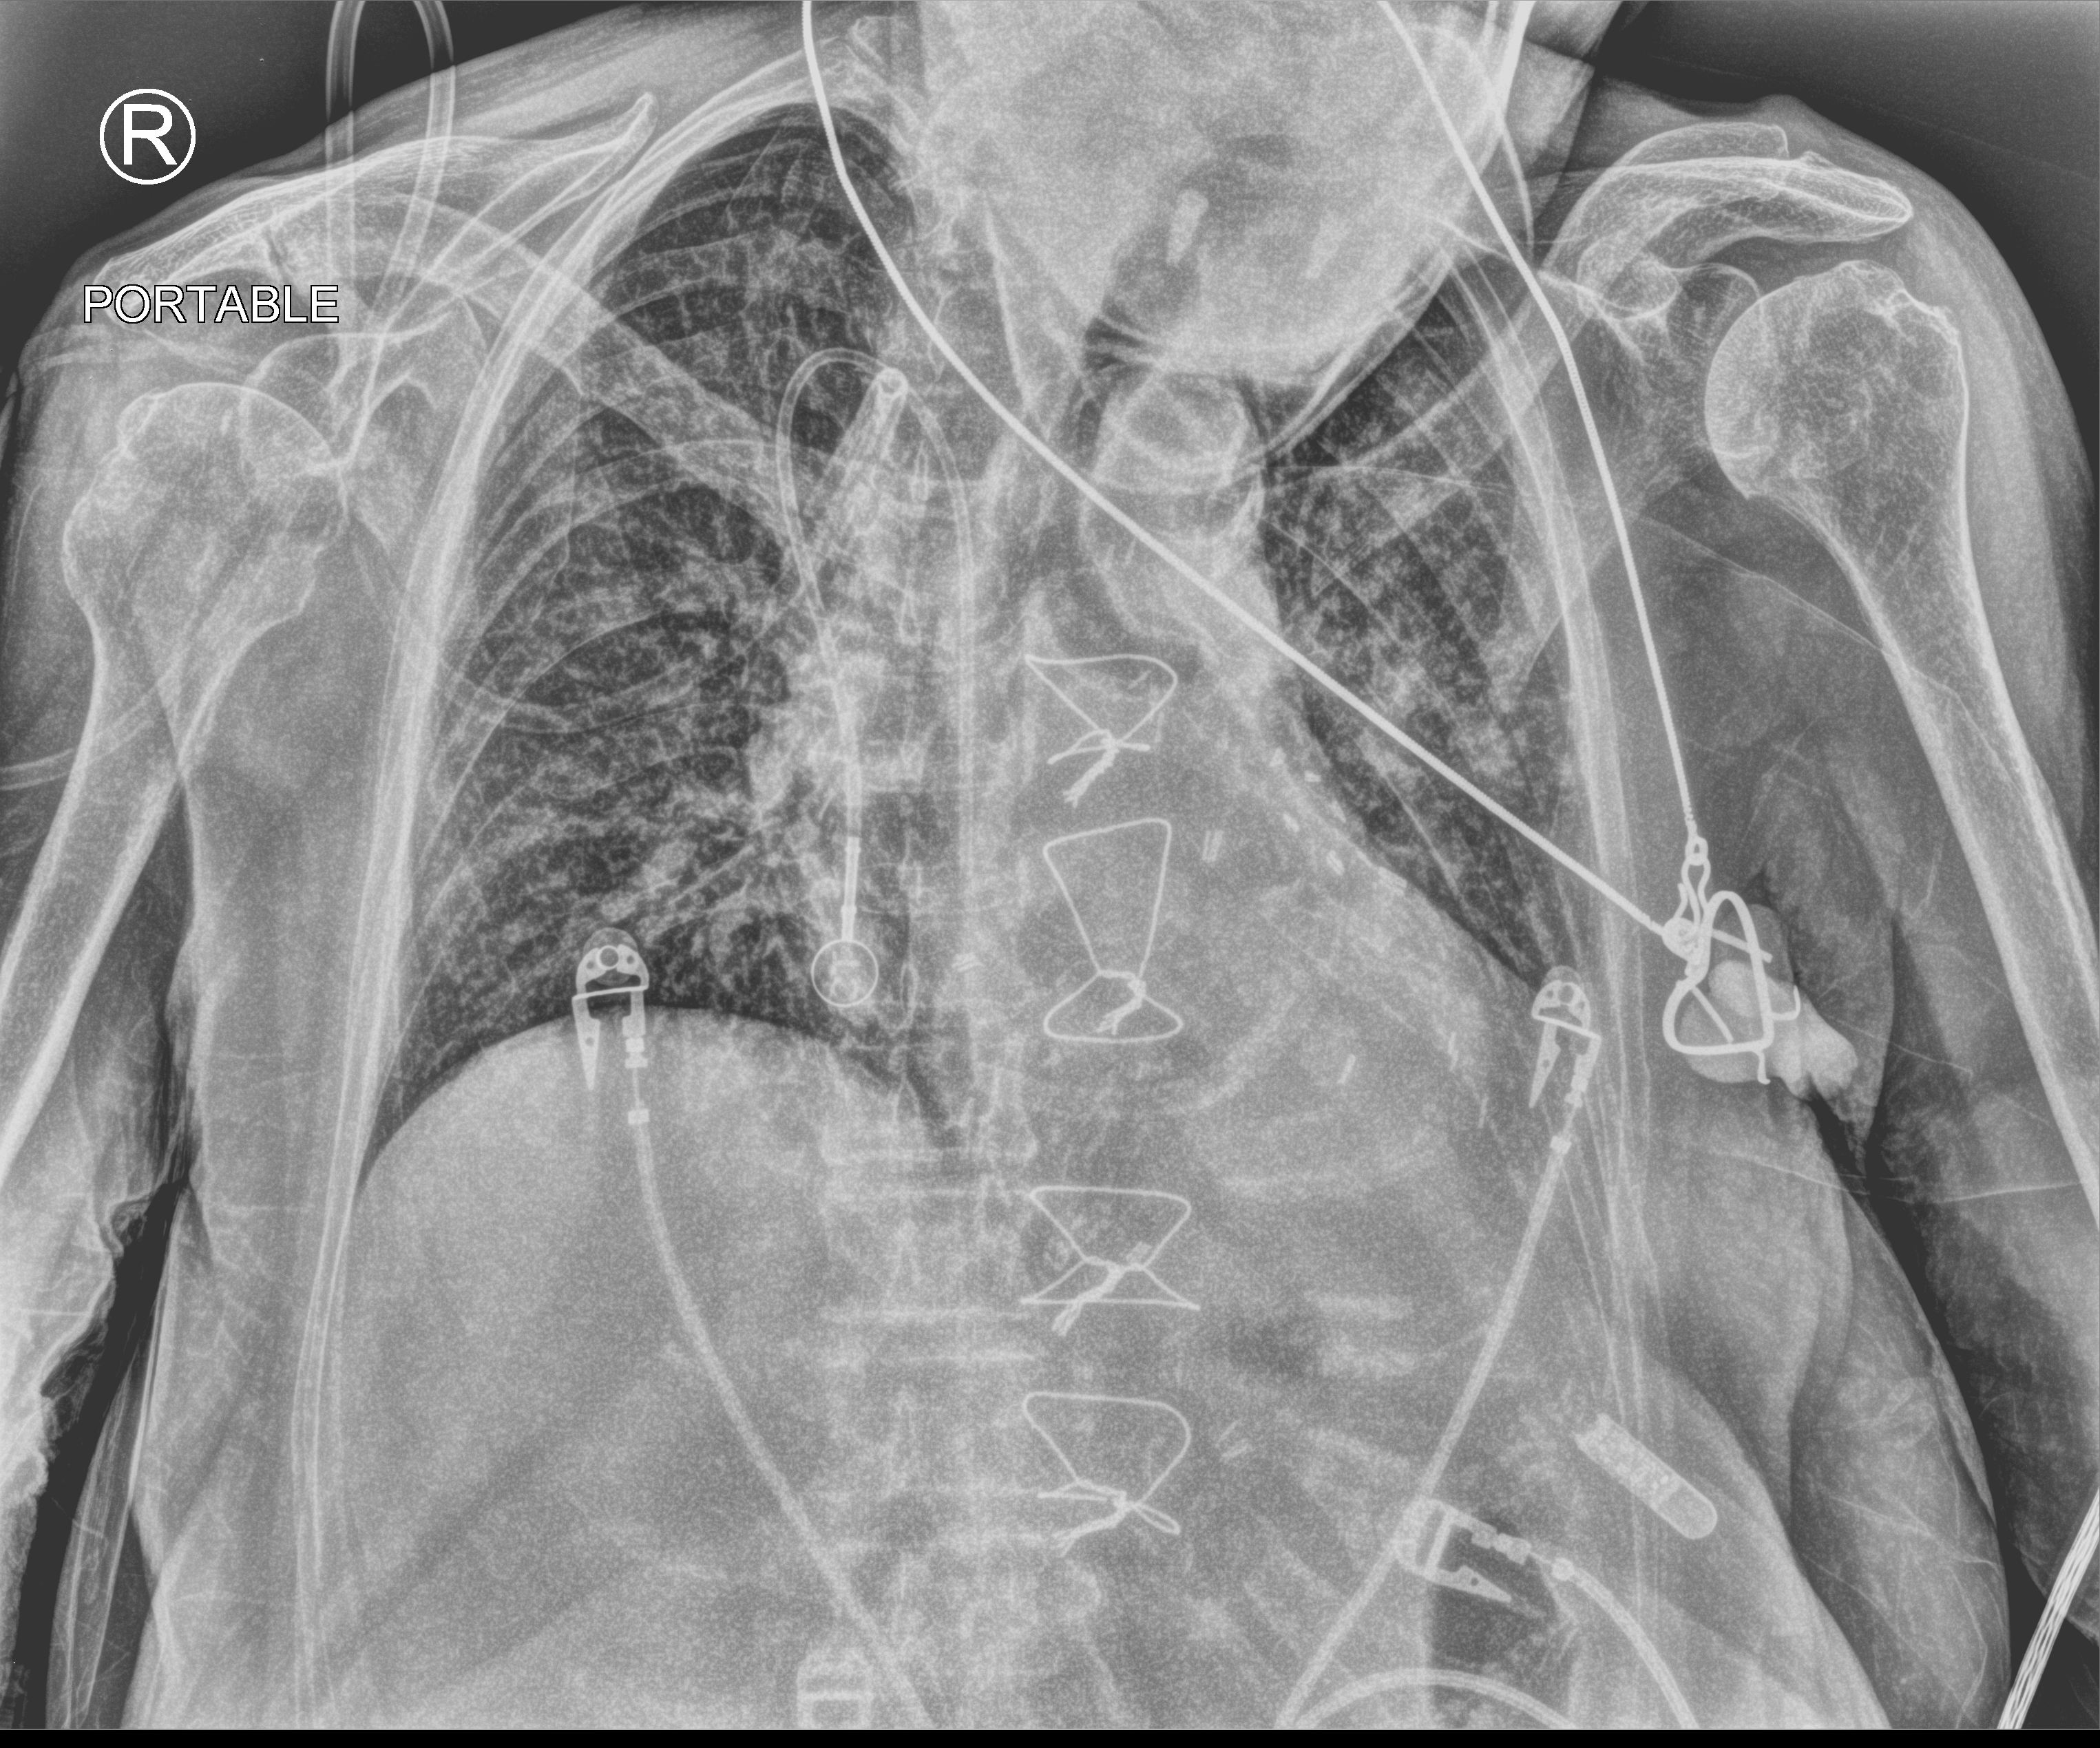
Chest X-ray (portable); anteroposterior (AP) projection. Patient hospitalised with COVID-19; female, aged 75–90 years.
Admission-level facts for this patient (not findings on this image; timing relative to this image not recorded): mechanically ventilated during this hospital stay: no.